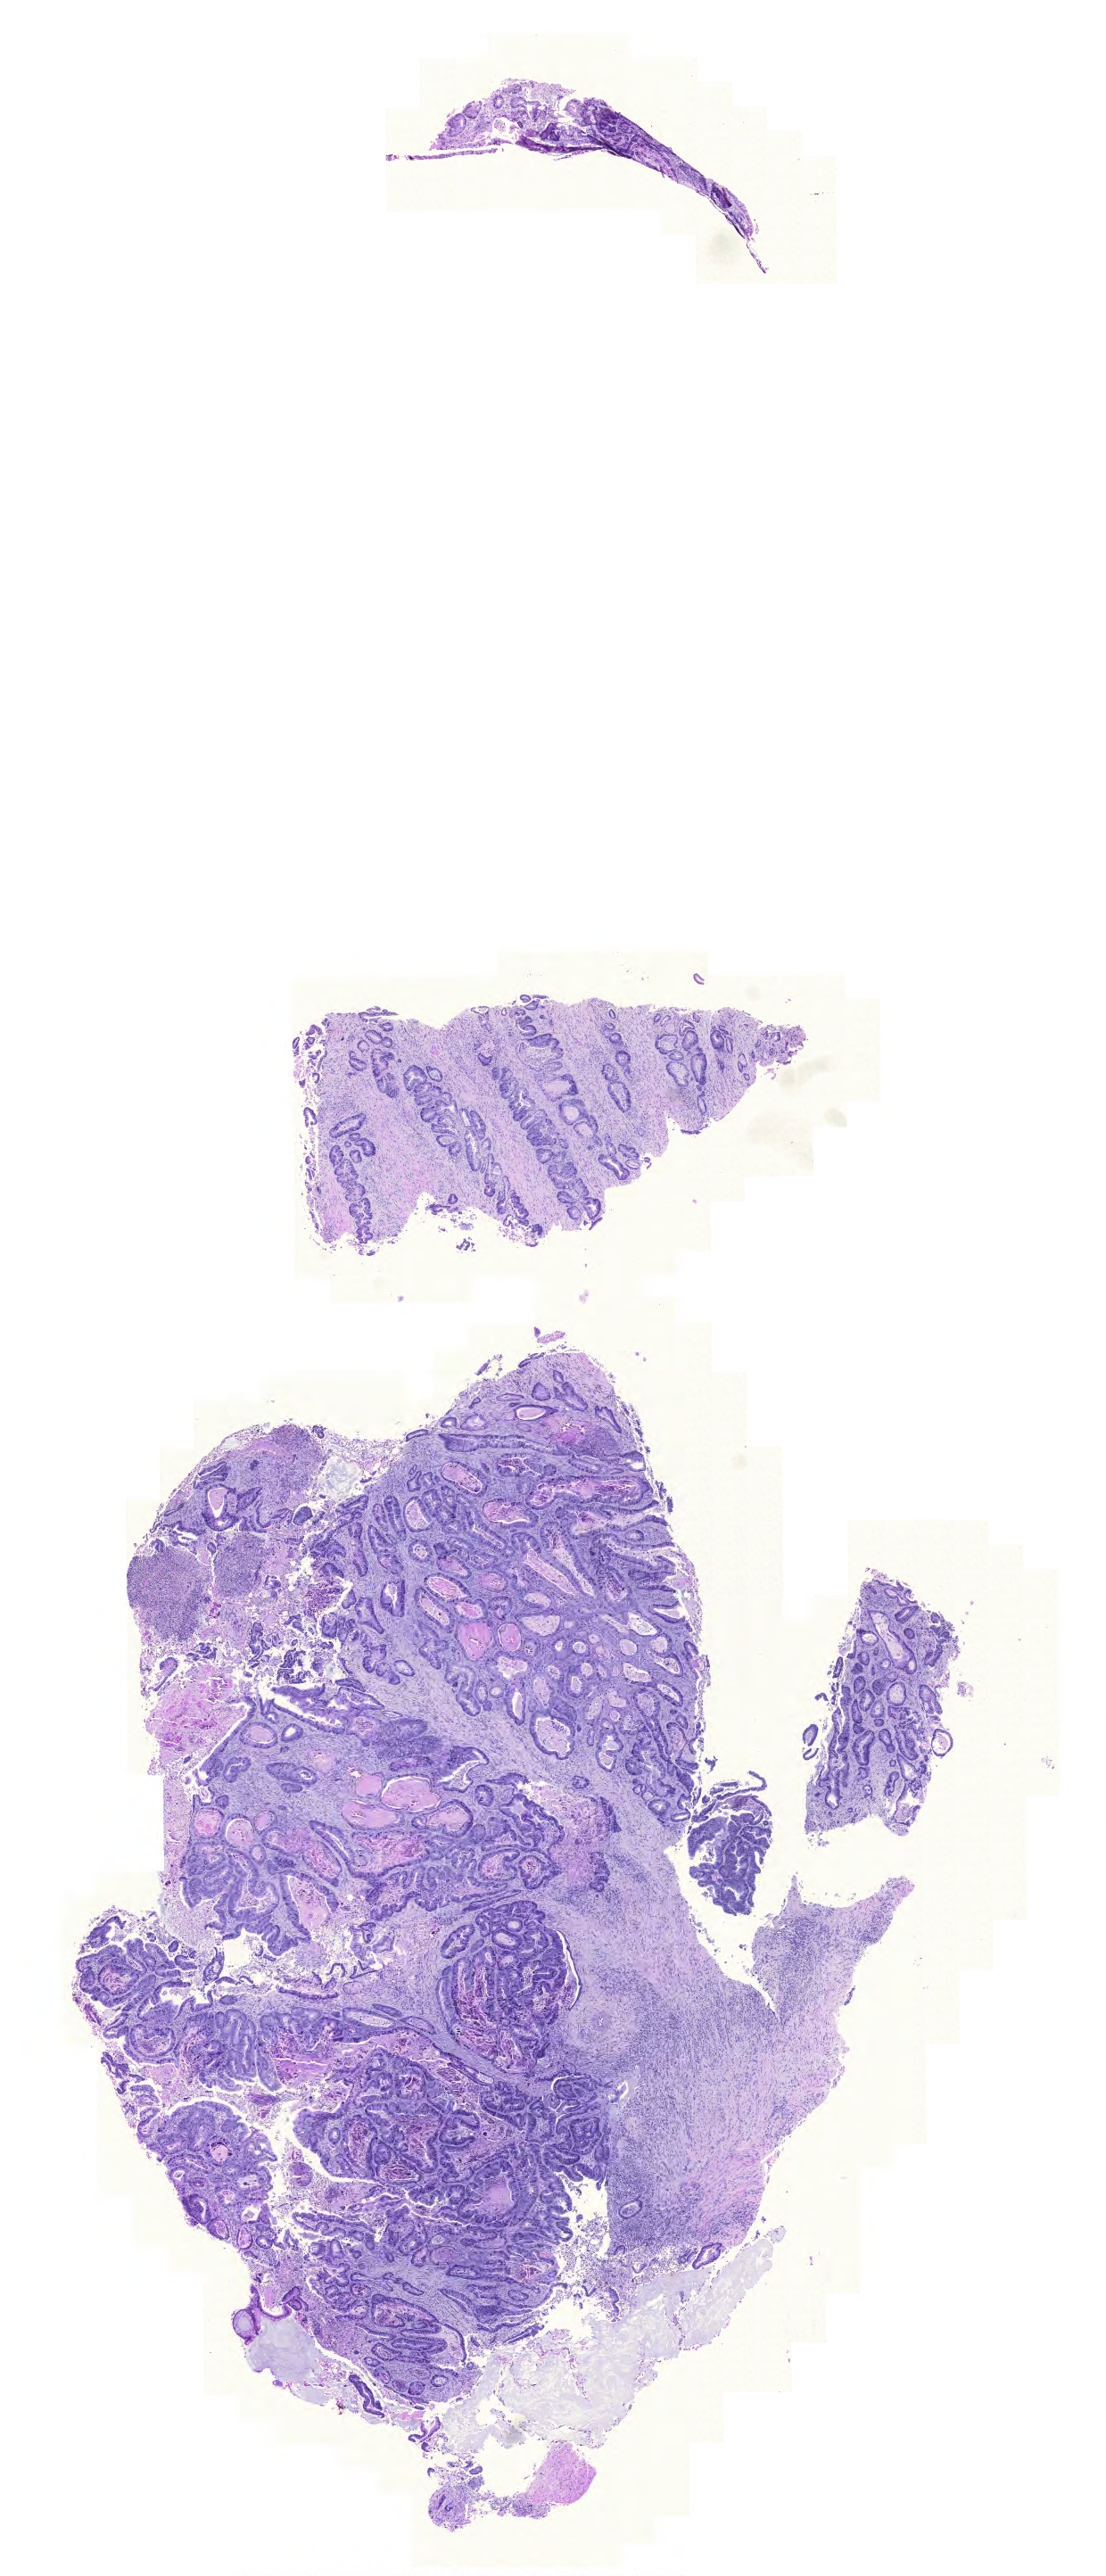
Hematoxylin and eosin (H&E) stained whole-slide image, a low-resolution overview of the entire scanned area, about 9.2 x 21.5 mm (acquisition: 20x scan). Formalin-fixed paraffin-embedded (FFPE) diagnostic section. Rectum, primary tumour sample. Female patient; age at initial diagnosis 65 years.
Diagnosis: Adenocarcinoma, NOS (rectosigmoid junction).